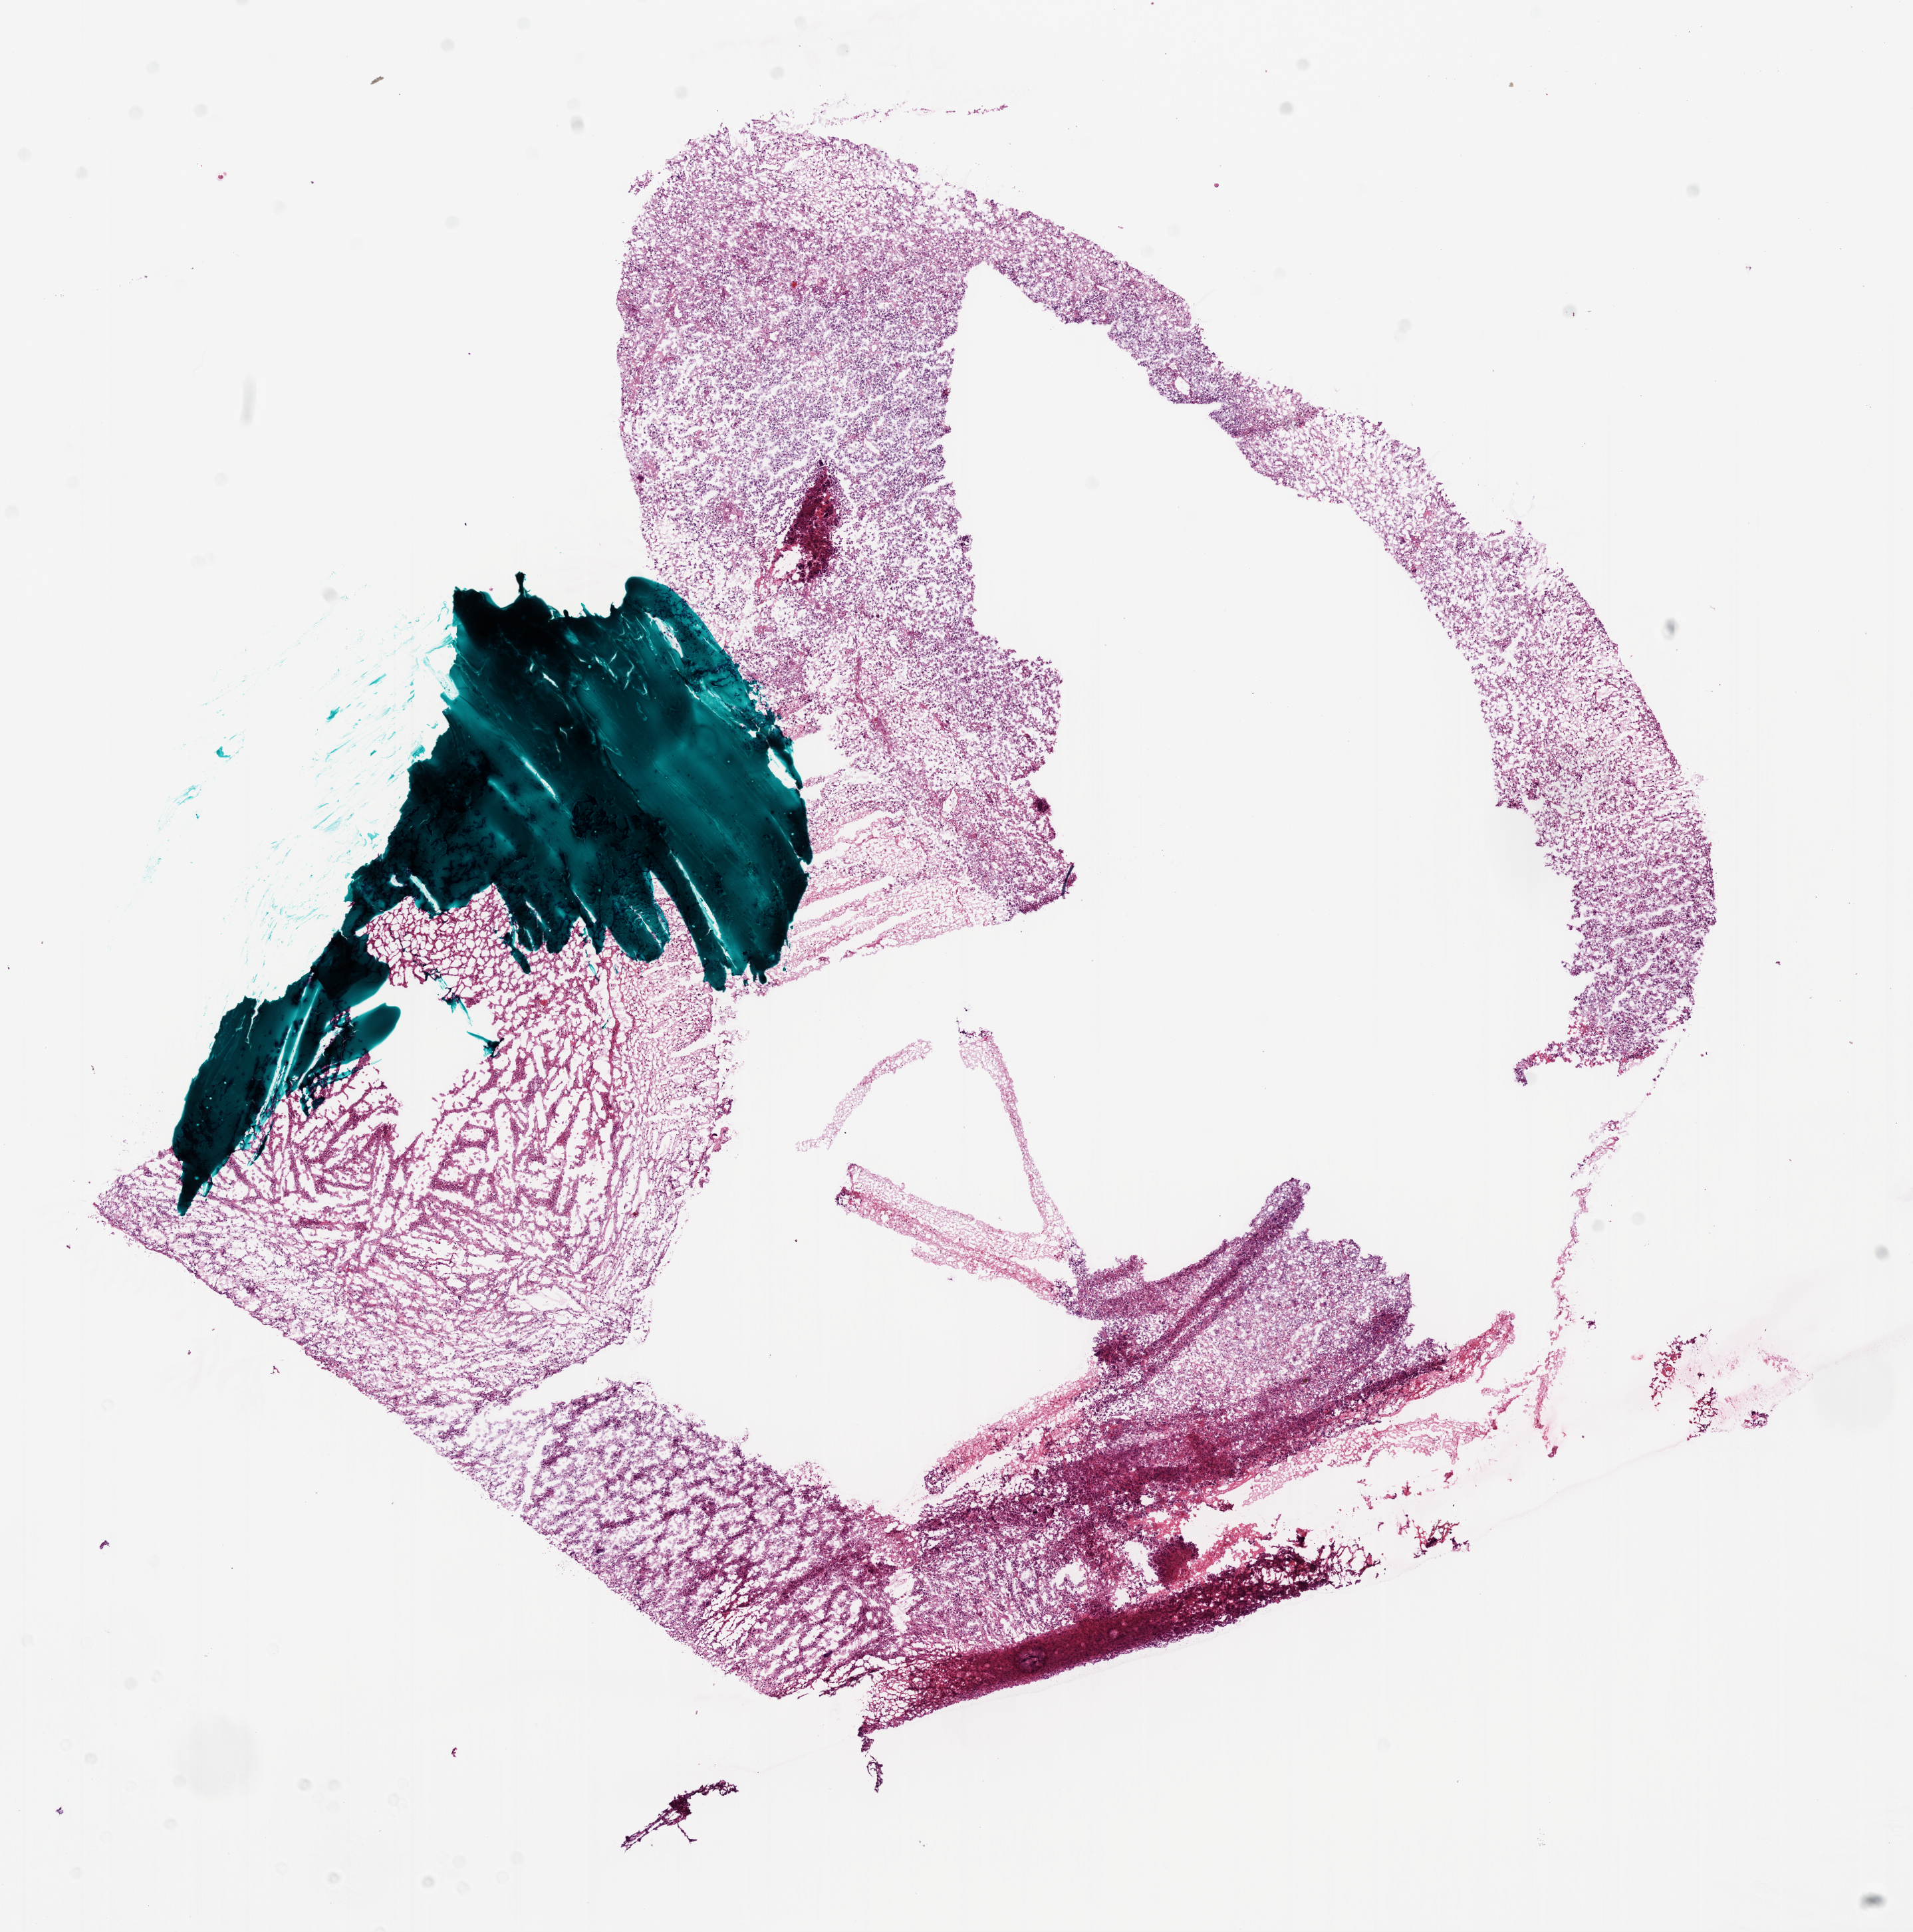
Whole-slide histology image, Hematoxylin and eosin (H&E) stained — a low-resolution overview of the entire scanned area, about 11.6 x 11.7 mm; frozen section; sample: primary tumour, brain. Male patient; age at initial diagnosis 51 years. Composition of this section per pathologist review: tumour cells 80%, tumour nuclei 100%, normal cells 0%, stromal cells 0%, necrosis 20%.
Pathologic diagnosis: Glioblastoma.